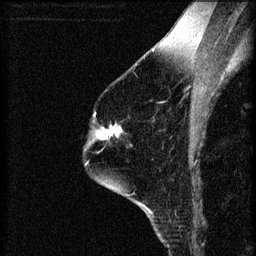
Breast MRI (dynamic contrast-enhanced), one sagittal slice; slice 44 of 60 in the series (ordered by position); 3 images stored at this slice position (order not interpretable as contrast timing); 1.5 T; TE 4.2 ms, TR 8.2 ms; 2 mm slice thickness; 256 × 256 image matrix, field of view 180 × 180 mm. Patient: female, 60 years.
Outlined on this slice (semi-automatic segmentation, software-assisted and operator-edited):
- analysis volume of interest (the breast-tissue region the enhancement analysis was run in; not a lesion): bounding box (x1, y1, x2, y2) in pixels: (89, 116, 122, 149)
- tumour enhancement mask (voxels above the 70 % enhancement threshold inside the analysis volume of interest): (93, 116, 122, 141)